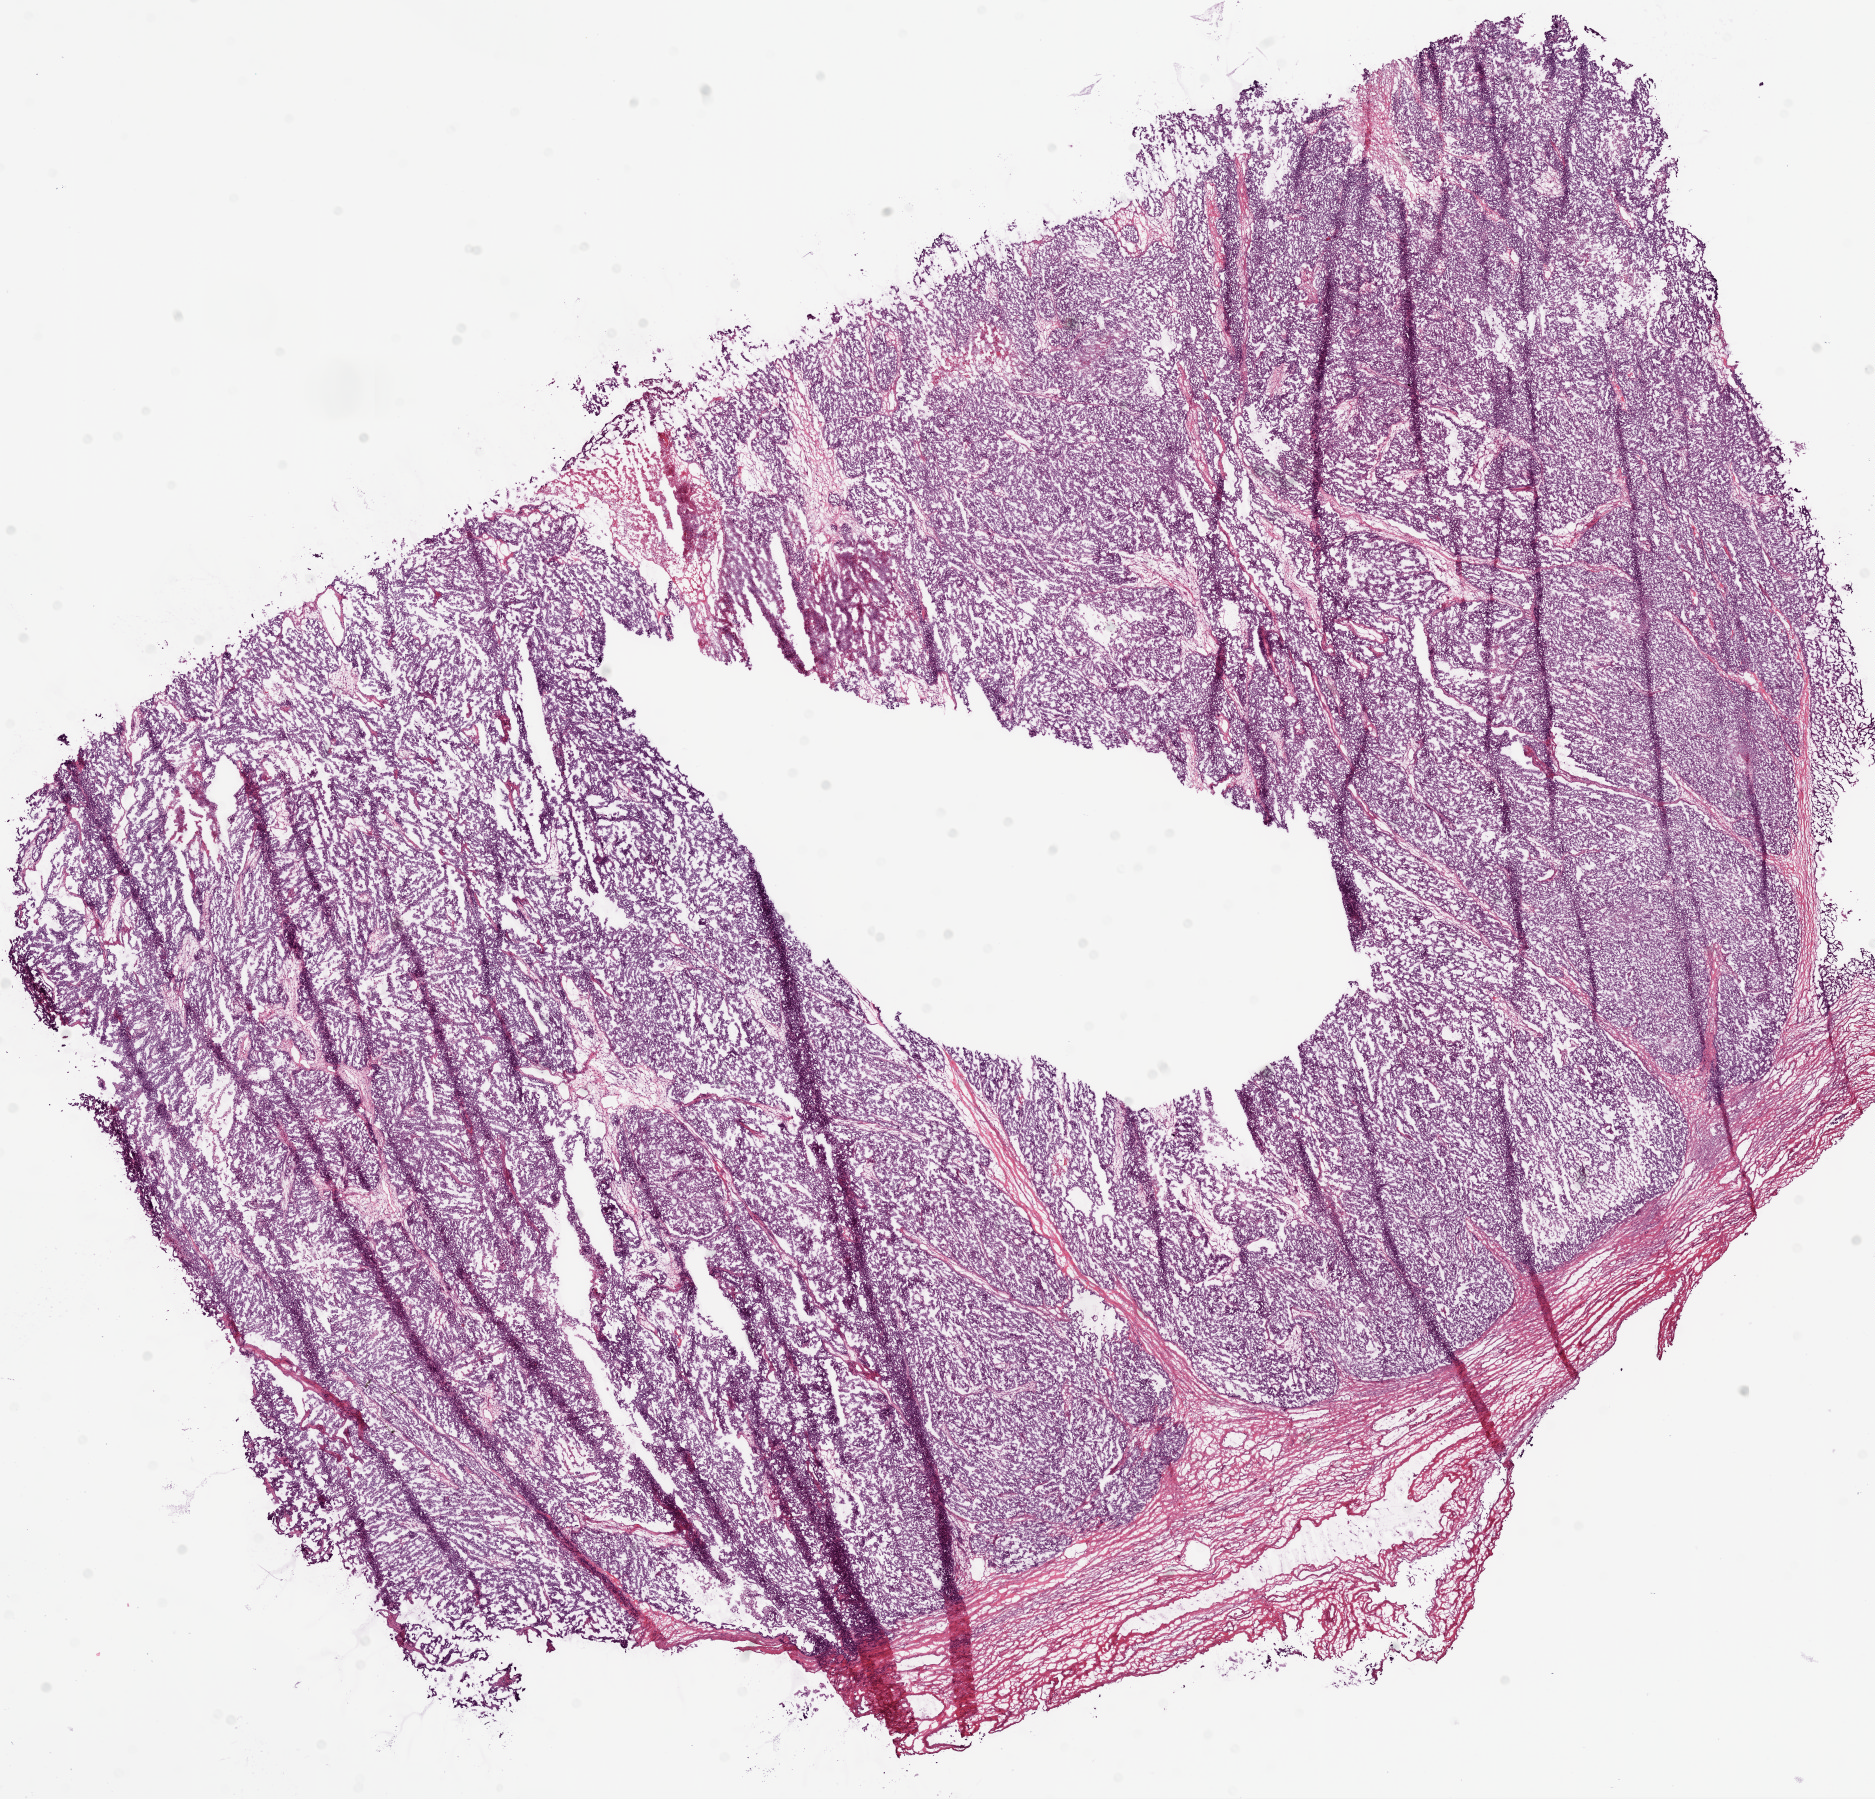
Digitized Hematoxylin and eosin (H&E) stained tissue section (whole slide), whole scanned area (about 15.0 x 14.4 mm) shown as a low-resolution overview. Frozen section from the bottom of the tissue portion. Ovary, primary tumour sample. Female patient; age at initial diagnosis 70 years. Histologic grade: G2 (moderately differentiated). Slide review estimates, as recorded: tumour cells 85%, tumour nuclei 95%, normal cells 5%, stromal cells 0%, necrosis 10%.
FIGO stage: IIIC. Diagnosis: Serous cystadenocarcinoma, NOS.